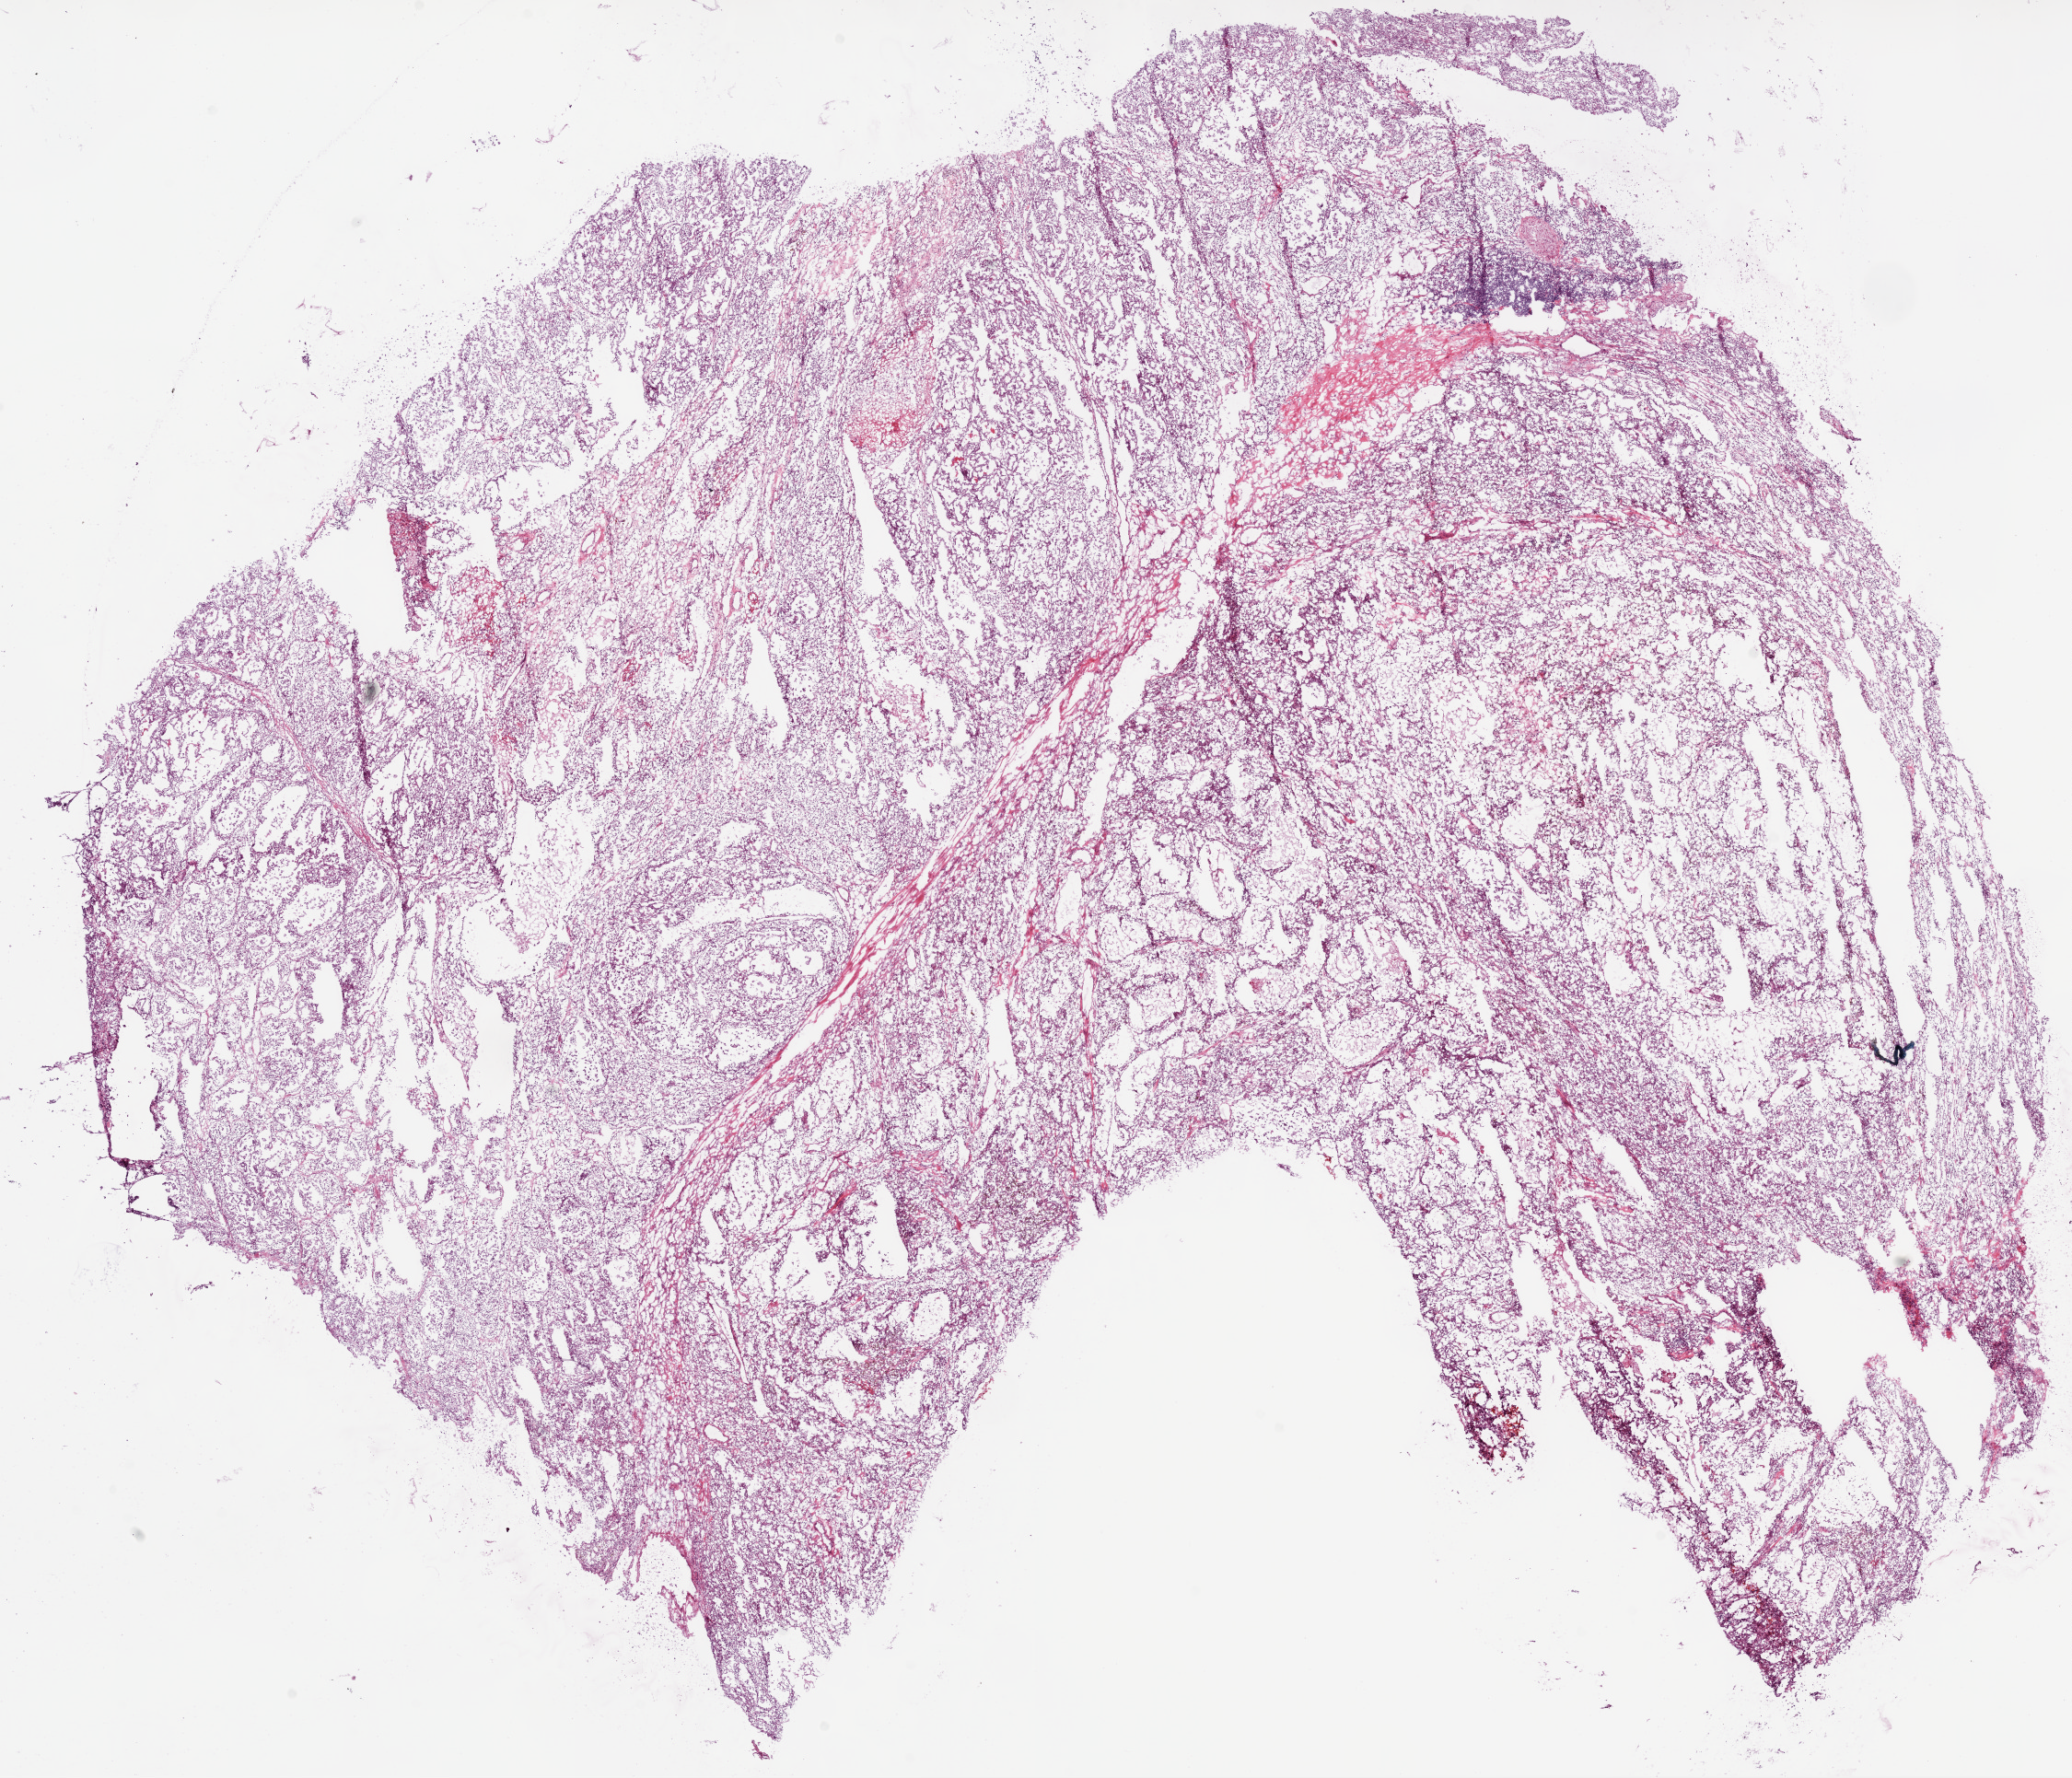
Hematoxylin and eosin (H&E) stained whole-slide image — low-resolution overview of the scanned area, about 18.1 x 15.5 mm (slide scanned at 20x). Frozen section from the bottom of the tissue portion. Primary tumour sample from the kidney. Male, age 53 years at initial diagnosis.
Pathologic diagnosis: Clear cell adenocarcinoma, NOS.